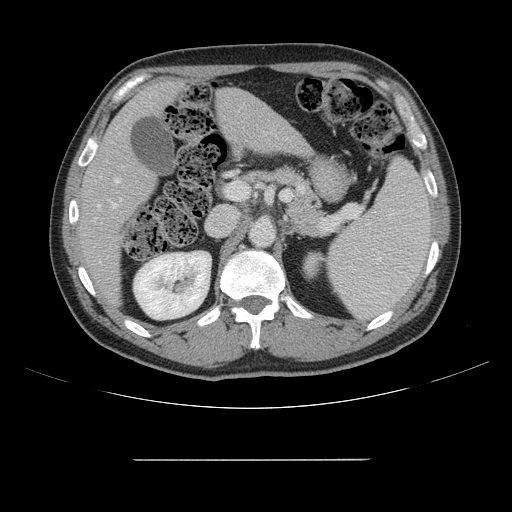
Contrast-enhanced abdominal CT, one axial slice; slice 84 of 164 in the series (ordered by position); intravenous contrast given; soft-tissue window (W 400 / L 40 HU); 2.5 mm slice thickness; 512 × 512 image matrix. Male patient, age 54 years. From the clinical record (not read from this slice): diagnosis: colorectal cancer liver metastases, imaged before liver resection; multiple liver metastases: yes; largest metastasis: 1 cm.
Annotated regions visible in this slice (expert manual segmentation):
- hepatic veins: bounding box (x1, y1, x2, y2) in pixels: (97, 178, 119, 263)
- liver: (82, 83, 306, 298)
- planned liver remnant (the part of the liver to remain after resection): (81, 83, 227, 300)
- portal vein (with intrahepatic branches): (112, 199, 122, 209)